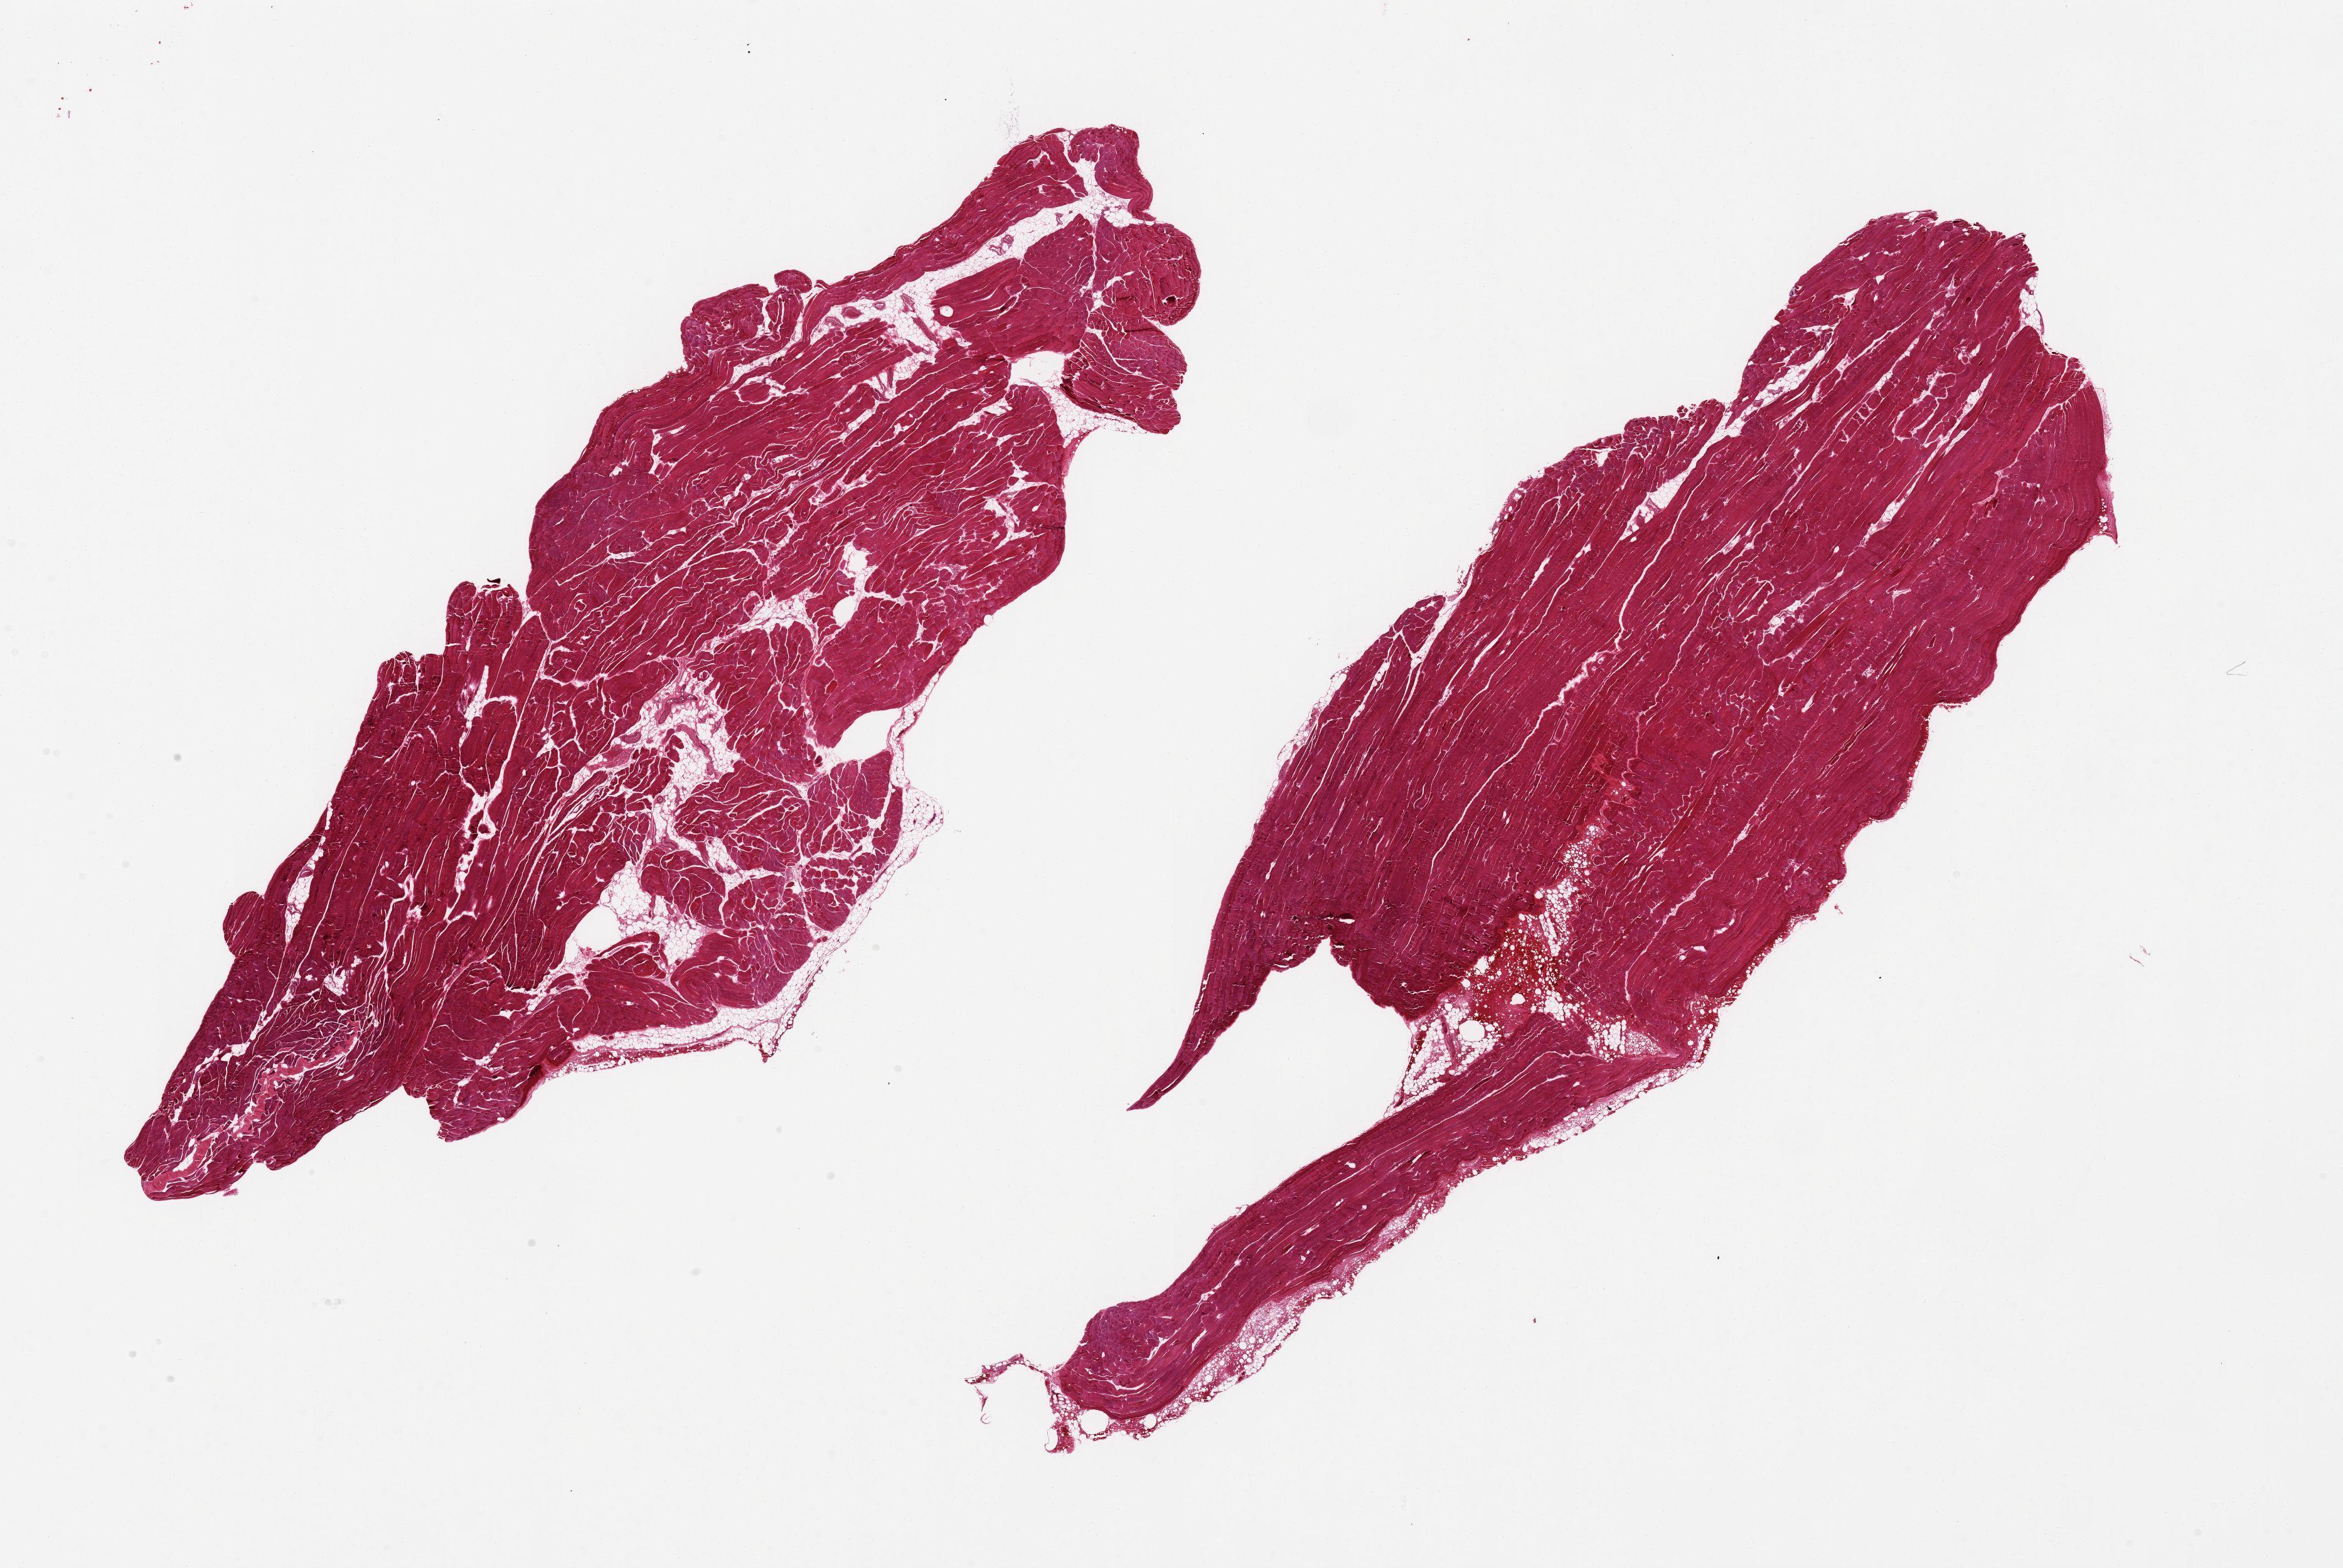
Hematoxylin and eosin (H&E) whole-slide image, whole scanned area (about 29.5 x 19.8 mm, from a 20x scan) shown as a low-resolution overview, PAXgene-fixed paraffin-embedded (PFPE) section, target tissue: skeletal muscle, tissue donor sample. Male donor.
Review note (as recorded): 2 pieces, includes up to 10% attached and internal adipose tissue.